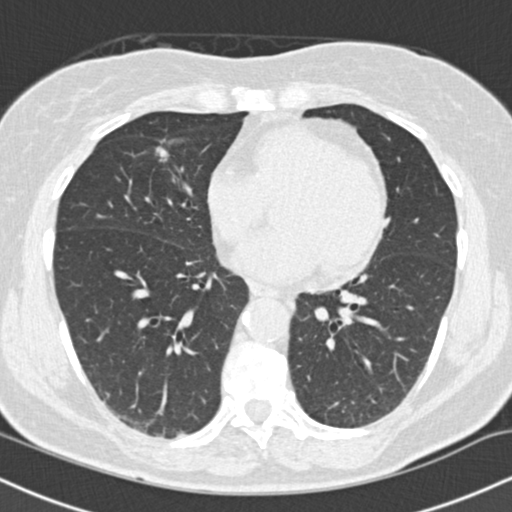
Chest CT (low-dose screening protocol), one axial image, first (baseline) screen, lung window (W 1500 / L -600 HU), standard (soft-tissue) reconstruction kernel (B30f), slice 84 of 145 in the series, 512 × 512 image matrix. Female, age 66 years at enrolment. Current smoker at enrolment.
Expert reader's lesion annotation, bounding box <138,138,181,173> (left, top, right, bottom; pixels). The exam's reader record, not a measurement of the box and not confirmed to be the same lesion: non-calcified nodule or mass ≥4 mm, right lower lobe, 10 × 8 mm, smooth margins, soft tissue attenuation. Official screen result: positive, change unspecified: nodule(s) >= 4 mm or enlarging nodule(s), mass(es), or other non-specific abnormalities suspicious for lung cancer. Participant outcome: lung cancer diagnosed 96 days after this screen — squamous cell carcinoma, keratinizing, NOS, right upper lobe, right middle lobe, poorly differentiated (G3), stage IA (AJCC 6th edition), 14 mm at pathology.